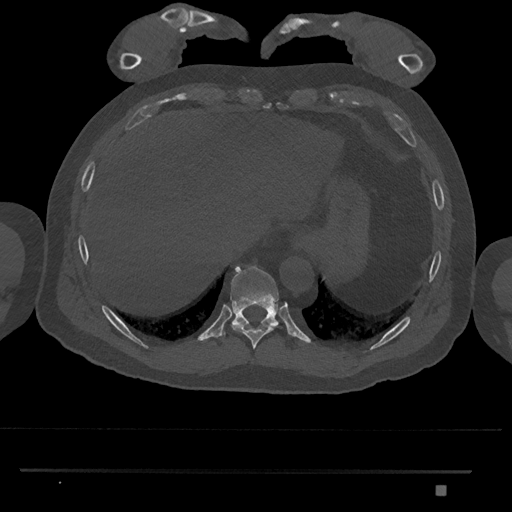
CT including the spine, one axial slice; slice 1029 of 1134 in the series (ordered by position); reconstruction kernel Br40s/3; bone window (W 1800 / L 400 HU); 512 × 512 image matrix, field of view 429 × 429 mm. Male patient, age 65 years. Case-level facts recorded for this patient, not image findings: primary cancer: prostate.
Structures marked on this image (semi-automatically segmented with operator editing):
- T10 vertebra: bounding box [x1, y1, x2, y2] px = [222, 264, 279, 337]
- T9 vertebra: [231, 323, 279, 349]